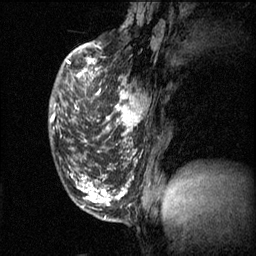
Breast MRI (dynamic contrast-enhanced), one sagittal slice. Position 19 of 60 along the scan axis. 3 images stored at this slice position (order not interpretable as contrast timing). 1.5 T. TE 4.2 ms, TR 11.1 ms. 2 mm slice thickness. 256 × 256 image matrix, field of view 180 × 180 mm. Patient: female, 50 years.
Outlined on this slice (semi-automatically segmented with operator editing):
- analysis volume of interest (the breast-tissue region the enhancement analysis was run in; not a lesion): bounding box <76,68,147,141> (left, top, right, bottom; pixels)
- tumour enhancement mask (voxels above the 70 % enhancement threshold inside the analysis volume of interest): <76,68,142,141>